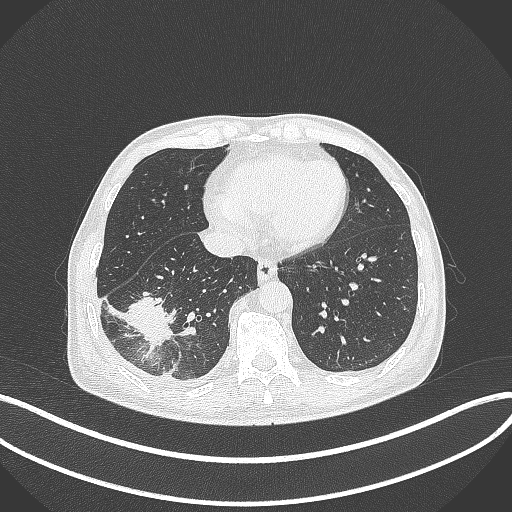
Chest CT, one axial slice; slice 112 of 388 in the series (ordered by position); reconstruction kernel B70f; lung window (W 1500 / L -600 HU); 512 × 512 image matrix. Male patient, age 64 years. Case-level facts recorded for this patient, not image findings: clinical TNM (as recorded): T3 N0 M0.
Outlined on this slice (bounding box drawn by a radiologist):
- lung tumour (recorded histology: adenocarcinoma): bounding box [x1, y1, x2, y2] px = [126, 292, 179, 354]